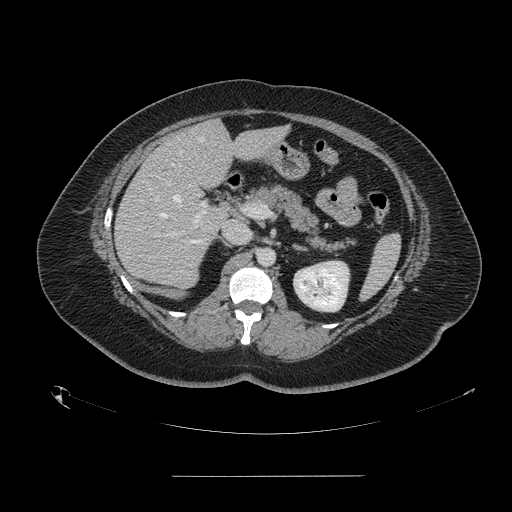
Contrast-enhanced abdominal CT, one axial slice; slice 83 of 164 in the series (ordered by position); intravenous contrast given; soft-tissue window (W 400 / L 40 HU); 2.5 mm slice thickness; 512 × 512 image matrix, field of view 495 × 495 mm. Female patient, age 52 years. From the clinical record (not read from this slice): diagnosis: colorectal cancer liver metastases, imaged before liver resection; multiple liver metastases: yes; largest metastasis: 3.5 cm; disease in both lobes: no.
Annotated regions visible in this slice (expert manual segmentation):
- hepatic veins: bounding box <155,137,203,218> (left, top, right, bottom; pixels)
- liver: <115,121,284,288>
- planned liver remnant (the part of the liver to remain after resection): <177,121,284,187>
- portal vein (with intrahepatic branches): <157,179,206,236>